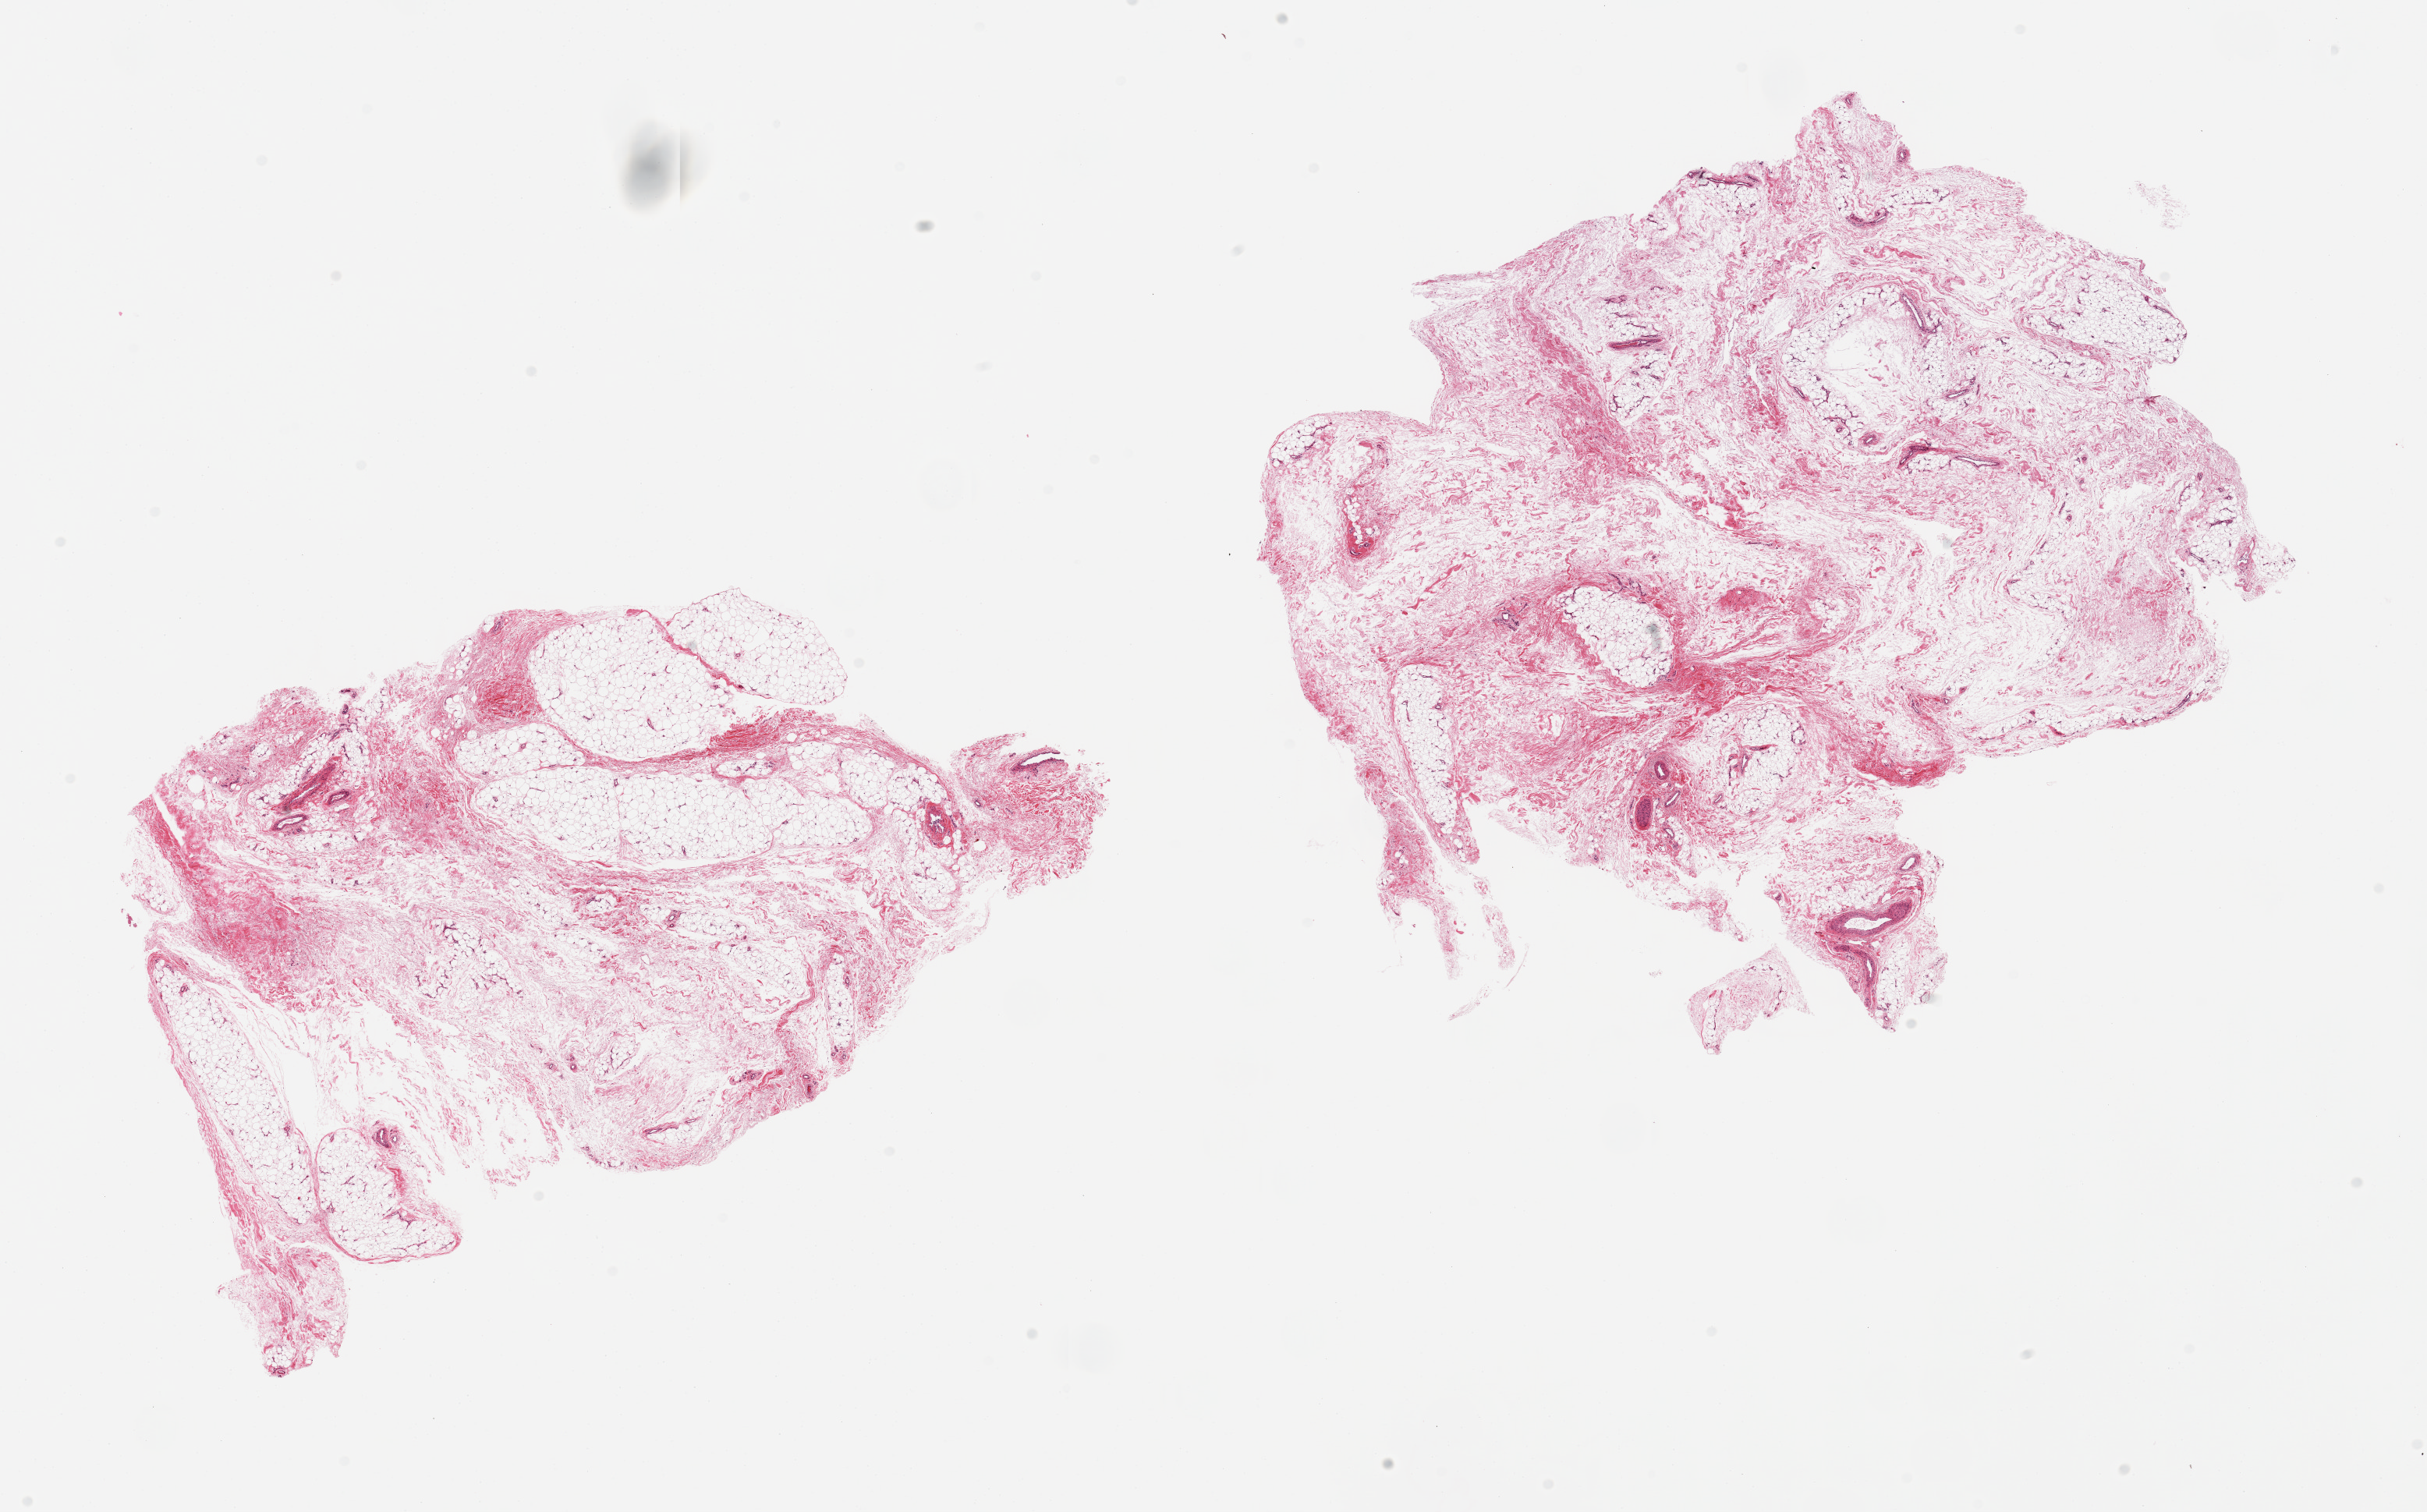
Whole-slide image, H&E stain, brightfield — whole scanned area (about 24.6 x 15.3 mm, acquisition: 20x scan) shown as a low-resolution overview; PAXgene-fixed paraffin-embedded (PFPE) section; target tissue: adipose tissue; tissue donor sample. Donor sex: male.
Review note (as recorded): 2 pieces, ~10-20% fibrovascular tissue intermingled.